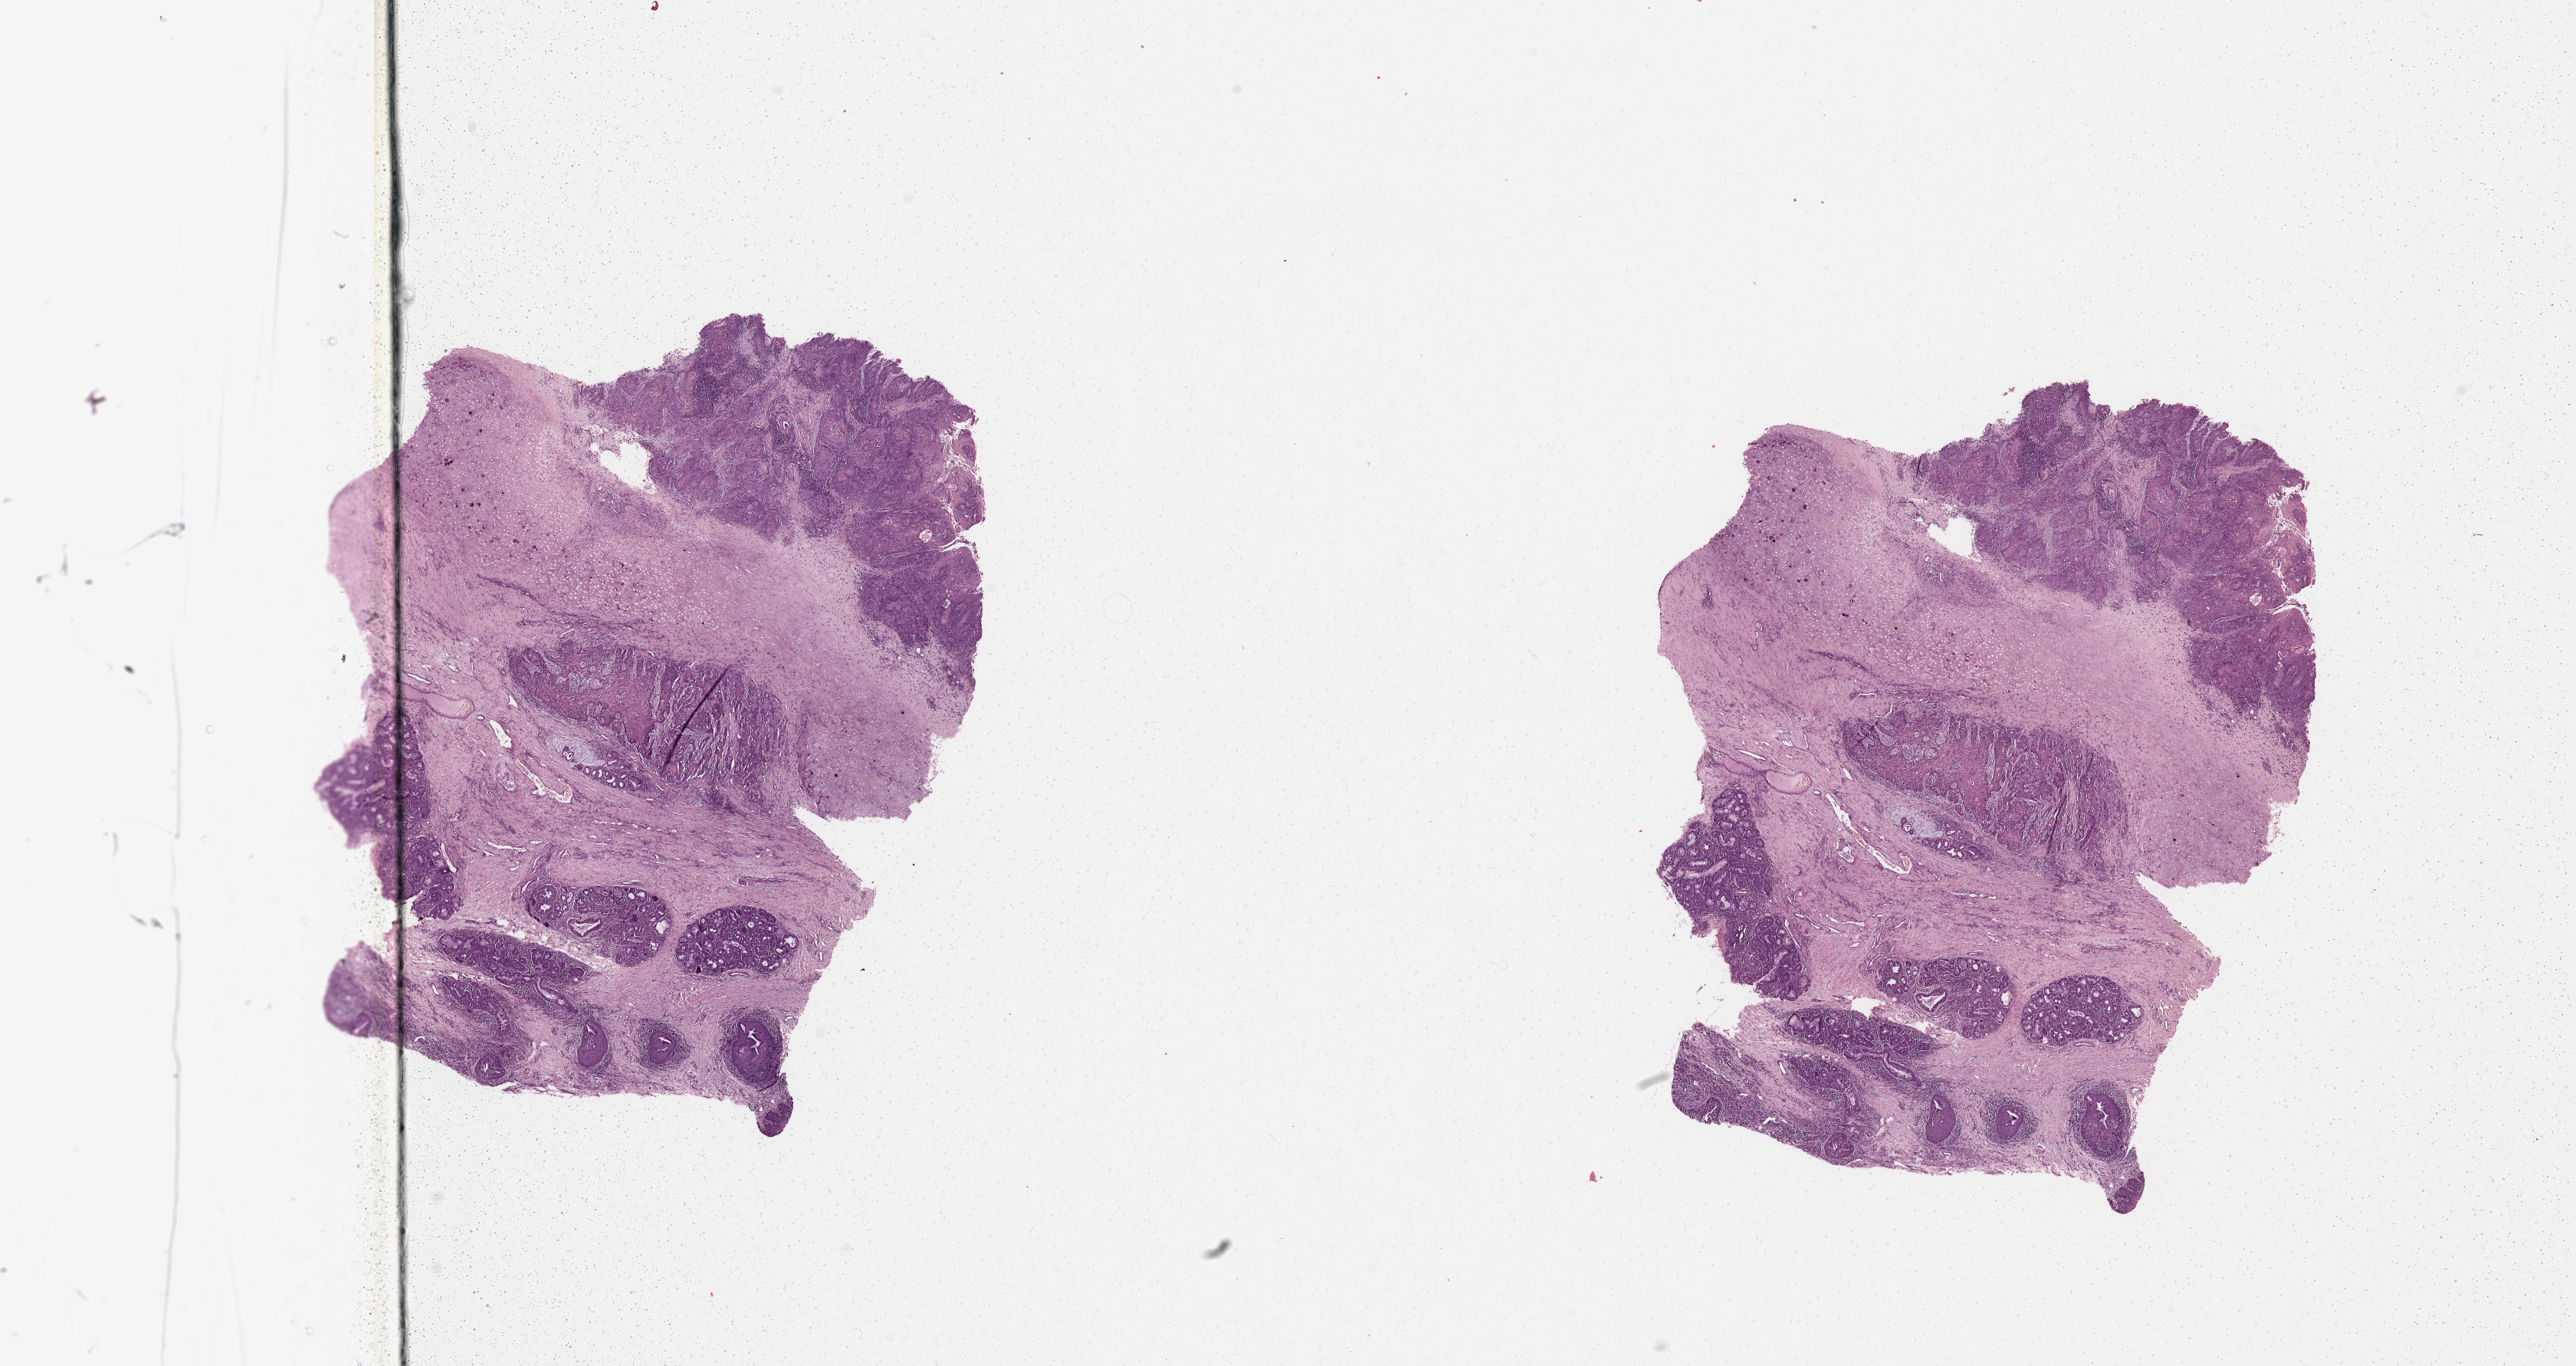
Hematoxylin and eosin (H&E) stained whole-slide image, low-resolution overview of the scanned area, about 26.6 x 14.1 mm; head and neck, tissue type not recorded. Patient: male, age 58 years.
Patient diagnosis: Squamous cell carcinoma, NOS.